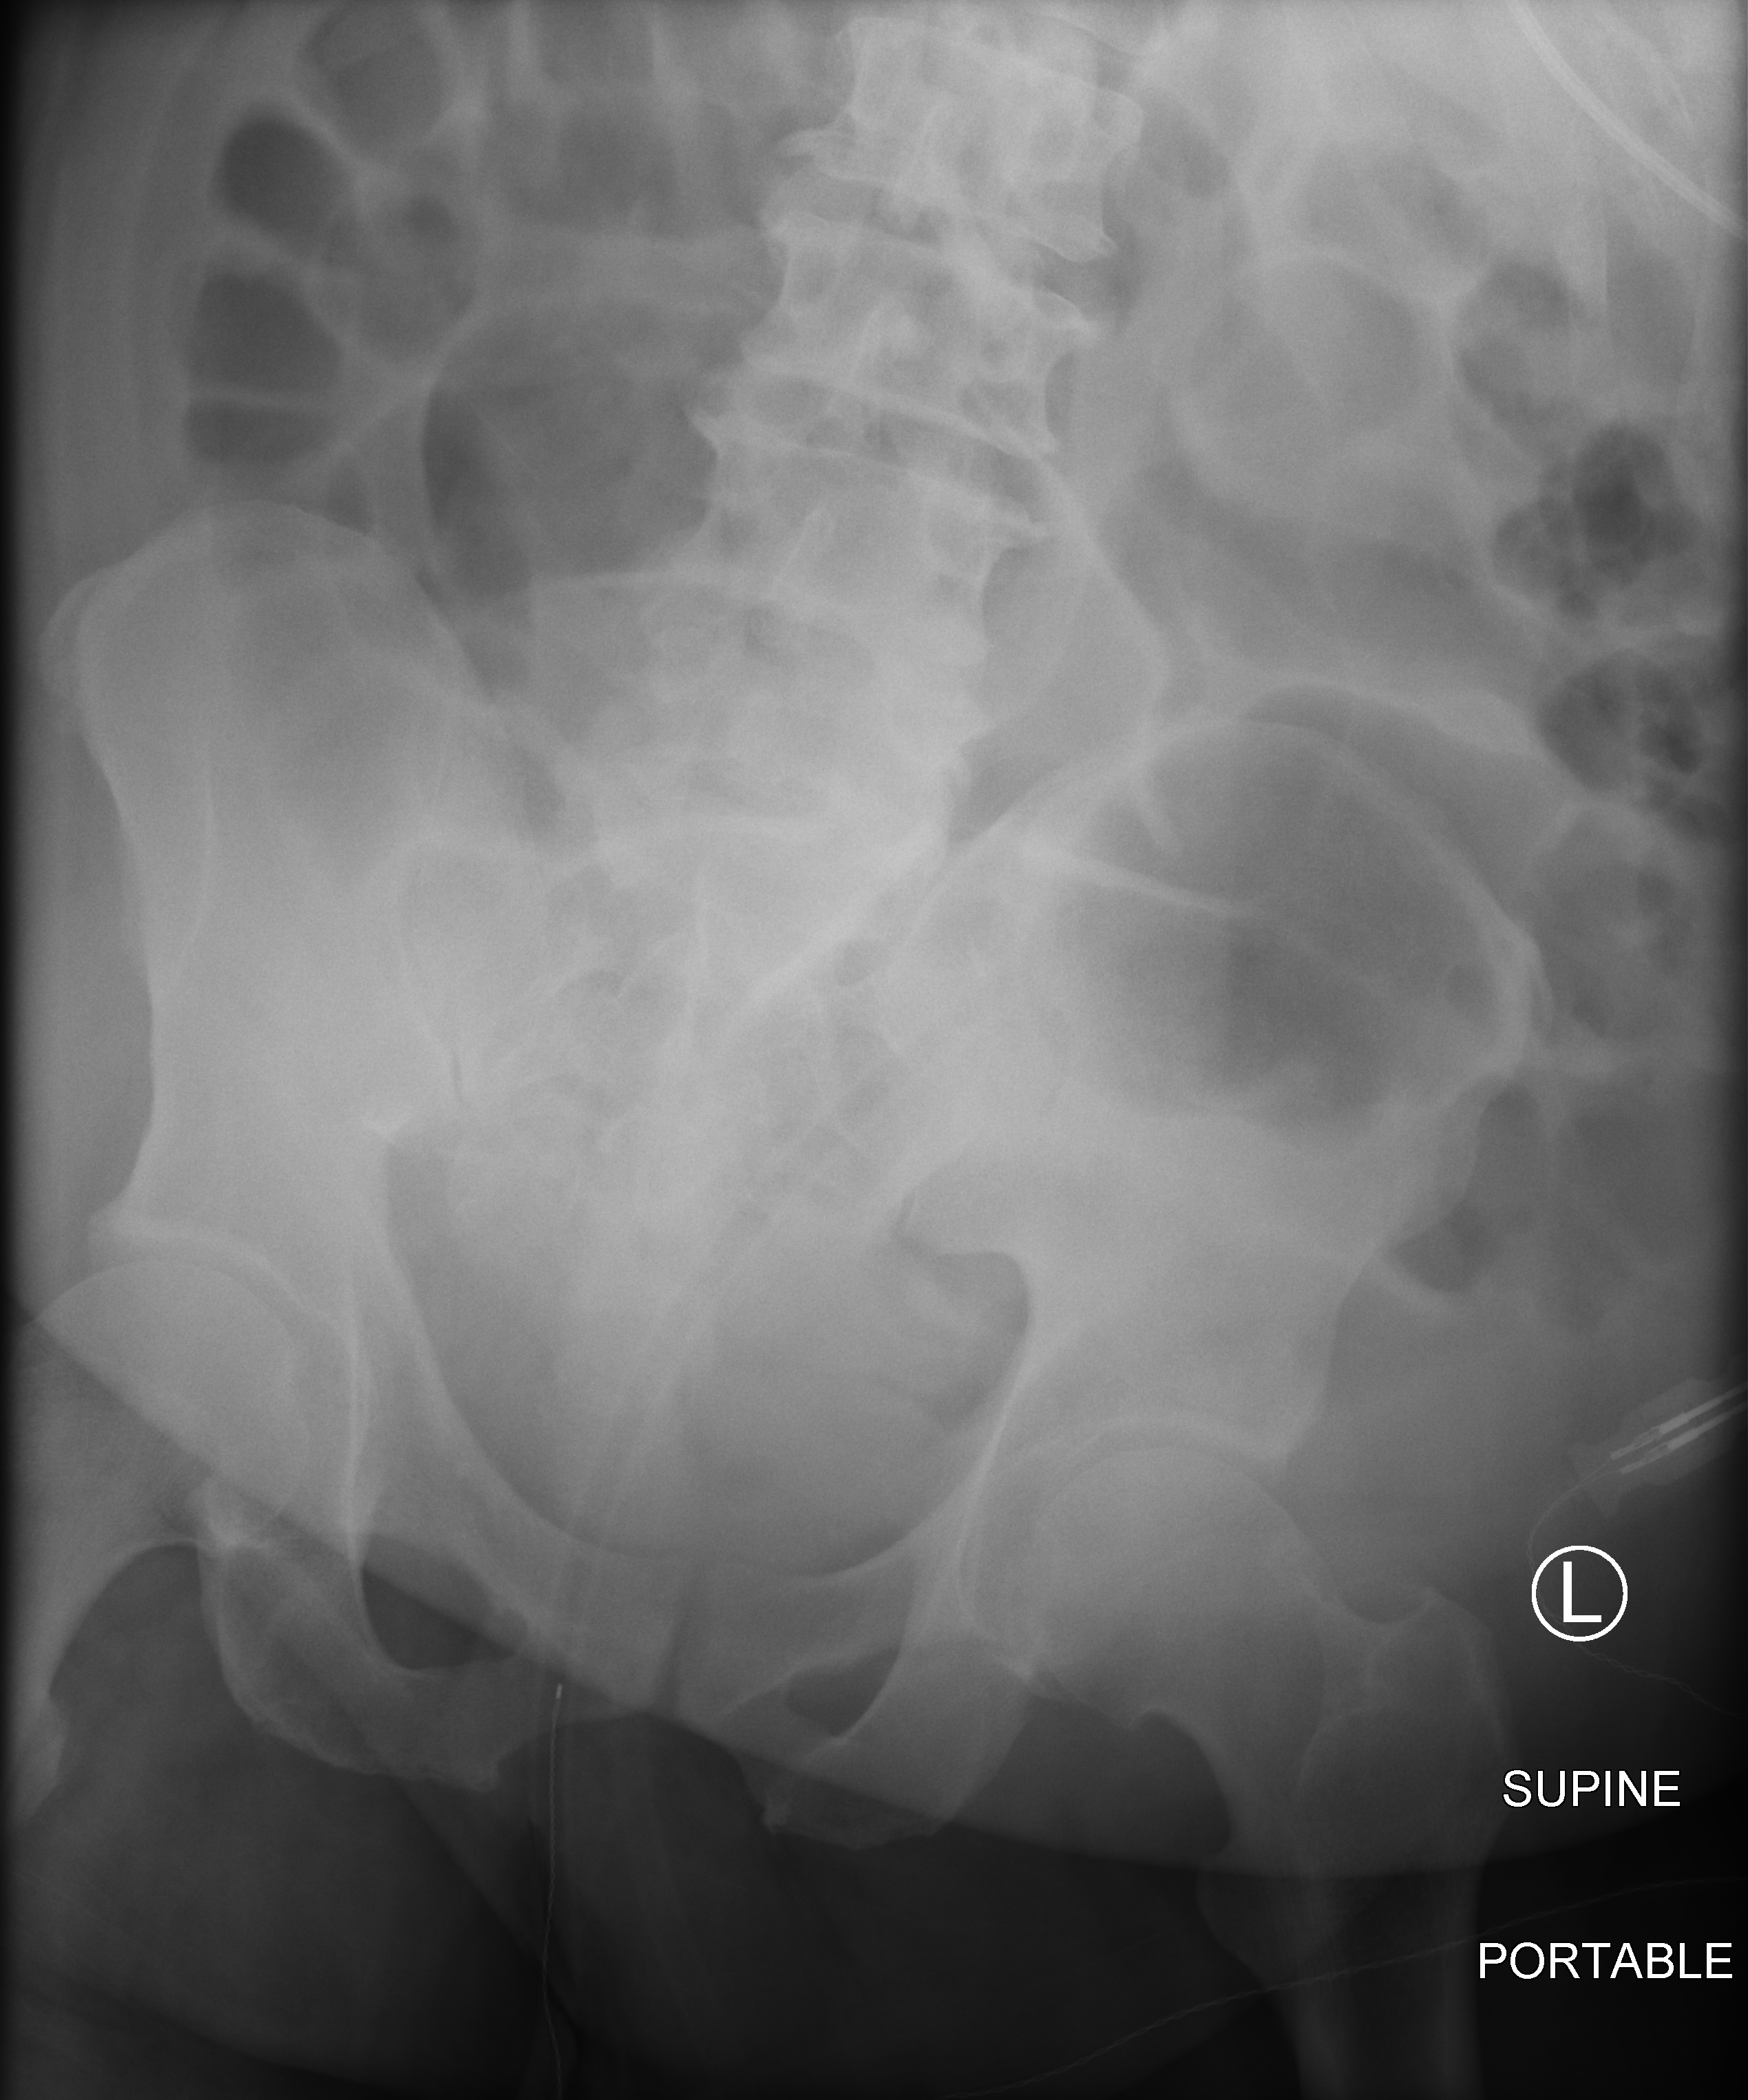
Abdomen X-ray (portable), anteroposterior (AP) projection. Male patient hospitalised with COVID-19, age 18–59 years.
Admission-level facts for this patient (not findings on this image; timing relative to this image not recorded): admitted to intensive care during this hospital stay: yes.